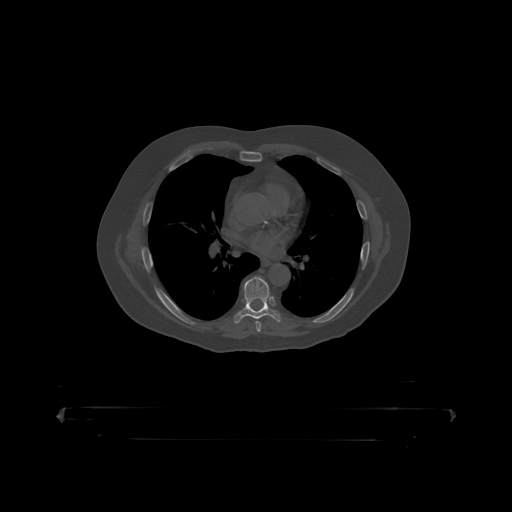
CT including the spine, one axial slice; slice 282 of 390 in the series (ordered by position); bone window (W 1800 / L 400 HU); 1.25 mm slice thickness; 512 × 512 image matrix, field of view 650 × 650 mm. Male patient, age 60 years. From the clinical record (not read from this slice): primary cancer: prostate.
Annotated regions visible in this slice (semi-automatically segmented with operator editing):
- T7 vertebra: bounding box (x1, y1, x2, y2) in pixels: (236, 277, 280, 319)